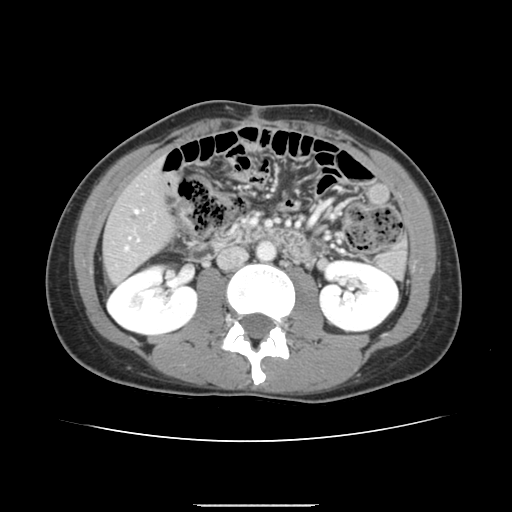
Contrast-enhanced abdominal CT, one axial slice; slice 52 of 150 in the series (ordered by position); 120 kVp; intravenous contrast given; soft-tissue window (W 400 / L 40 HU); 2.5 mm slice thickness; 512 × 512 image matrix. Female patient, age 32 years. Case-level facts recorded for this patient, not image findings: diagnosis: colorectal cancer liver metastases, imaged before liver resection; multiple liver metastases: yes; largest metastasis: 0.7 cm; chemotherapy before resection: yes.
Annotated regions visible in this slice (manually delineated by an expert):
- hepatic veins: box from (x=126, y=210) to (x=138, y=249) px
- liver: (x=104, y=165)–(x=172, y=282)
- planned liver remnant (the part of the liver to remain after resection): (x=104, y=164)–(x=172, y=282)
- portal vein (with intrahepatic branches): (x=137, y=239)–(x=139, y=241)